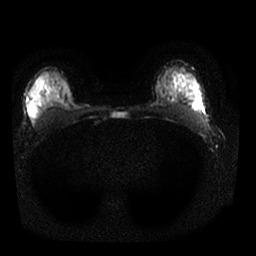
Breast MRI, one axial slice. Diffusion-weighted series; image 2 of 4 stored at this slice position (different b-values; order by instance number). 1.5 T. 256 × 256 image matrix, field of view 320 × 320 mm. Female patient.
Structures marked on this image (expert manual segmentation):
- tumour on diffusion-weighted imaging: bounding box <199,104,202,109> (left, top, right, bottom; pixels)